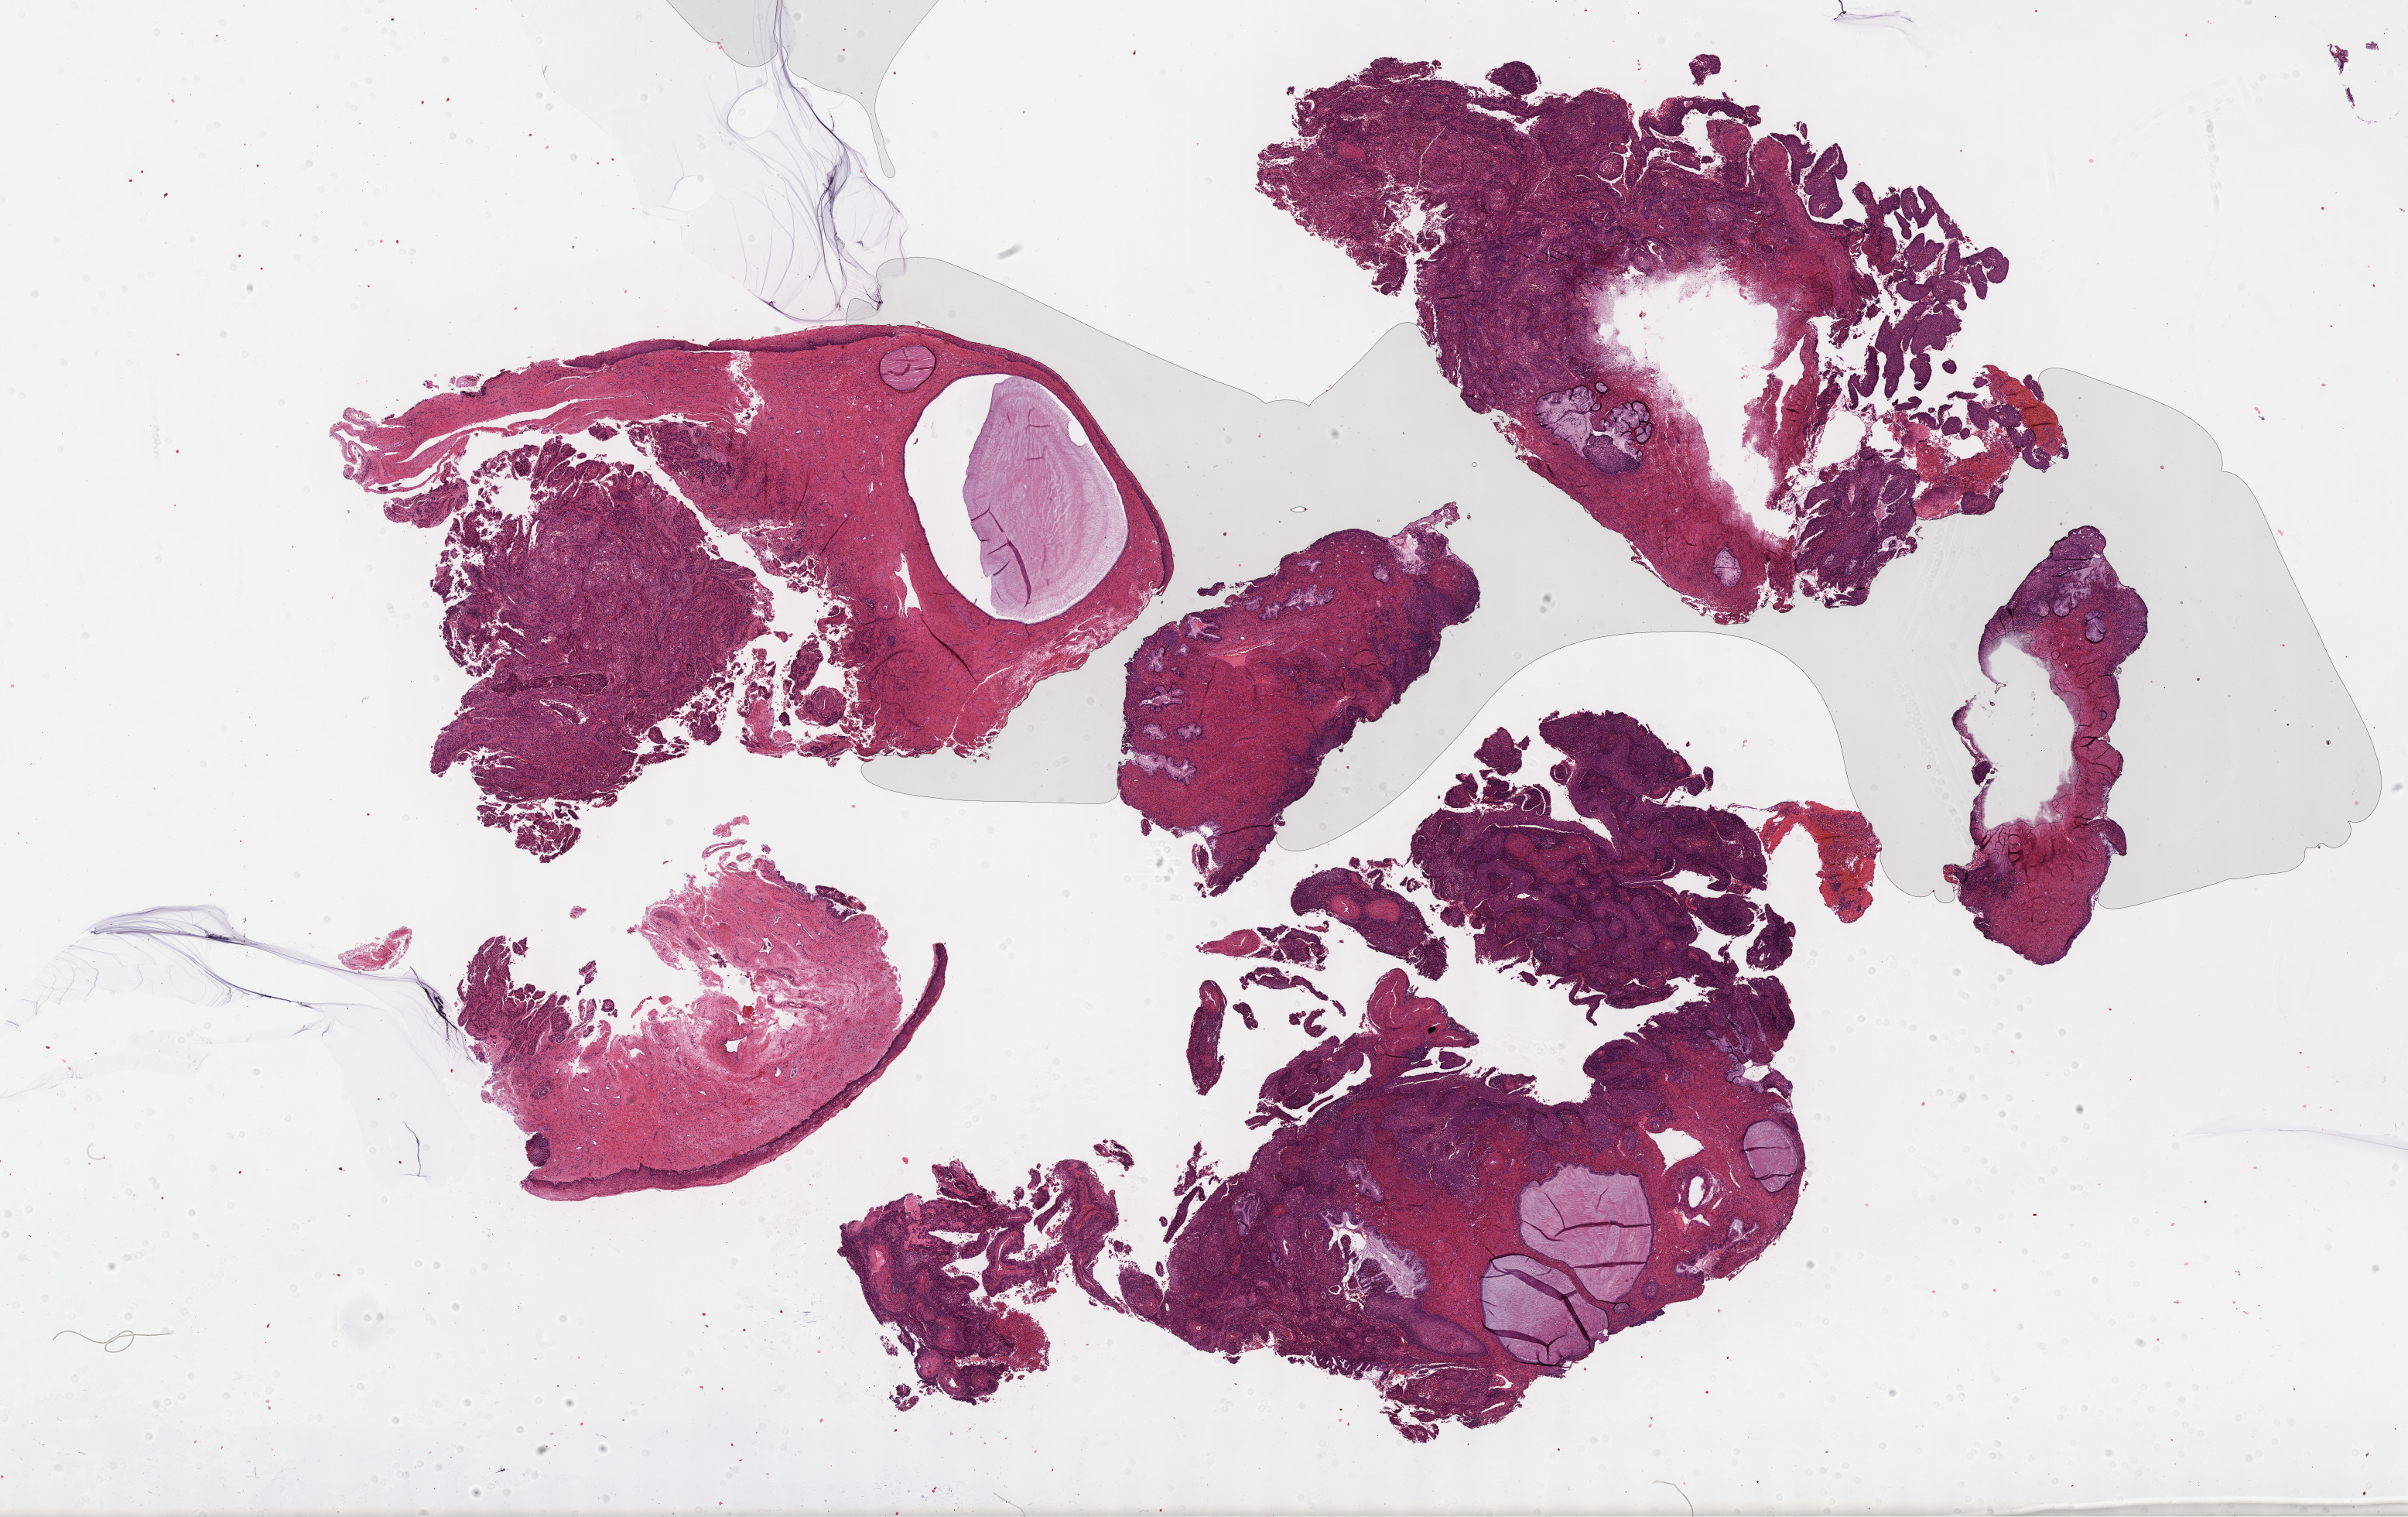
Digitized H&E tissue section (whole slide), shown as a low-resolution overview of the whole scanned area (about 25.2 x 15.9 mm), formalin-fixed paraffin-embedded (FFPE) diagnostic section, primary tumour sample from the cervix. Female, age 38 years at initial diagnosis.
Histologic diagnosis: Squamous cell carcinoma, keratinizing, NOS (cervix uteri).